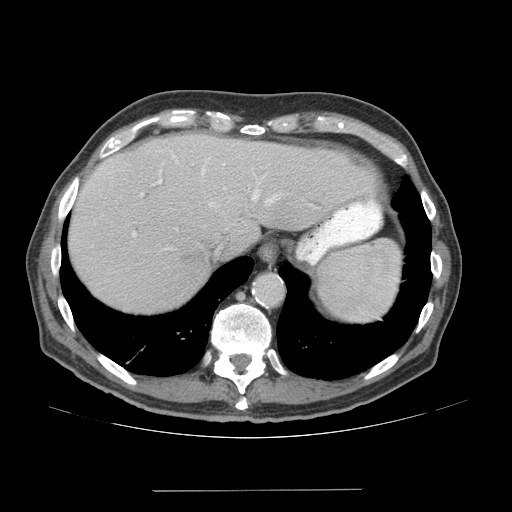
Contrast-enhanced abdominal CT (liver protocol), one axial slice. Slice 56 of 77 in the series (ordered by position). Reconstruction kernel STANDARD. Soft-tissue window (W 400 / L 40 HU). 512 × 512 image matrix, field of view 400 × 400 mm. From the clinical record (not read from this slice): diagnosis: hepatocellular carcinoma (patient treated with transarterial chemoembolisation; whether this scan precedes or follows treatment is not stated here); TNM stage (as recorded): Stage-IVA; Child-Pugh class: A; tumour differentiation: well differentiated; tumour nodularity: uninodular.
Outlined on this slice (semi-automatic segmentation, software-assisted and operator-edited):
- abdominal aorta: bounding box [x1, y1, x2, y2] px = [255, 275, 282, 305]
- liver parenchyma outside the tumour (the mass and vessels are separate outlines, so this box may not span the whole liver): [68, 134, 376, 312]
- liver vessels: [132, 155, 279, 236]